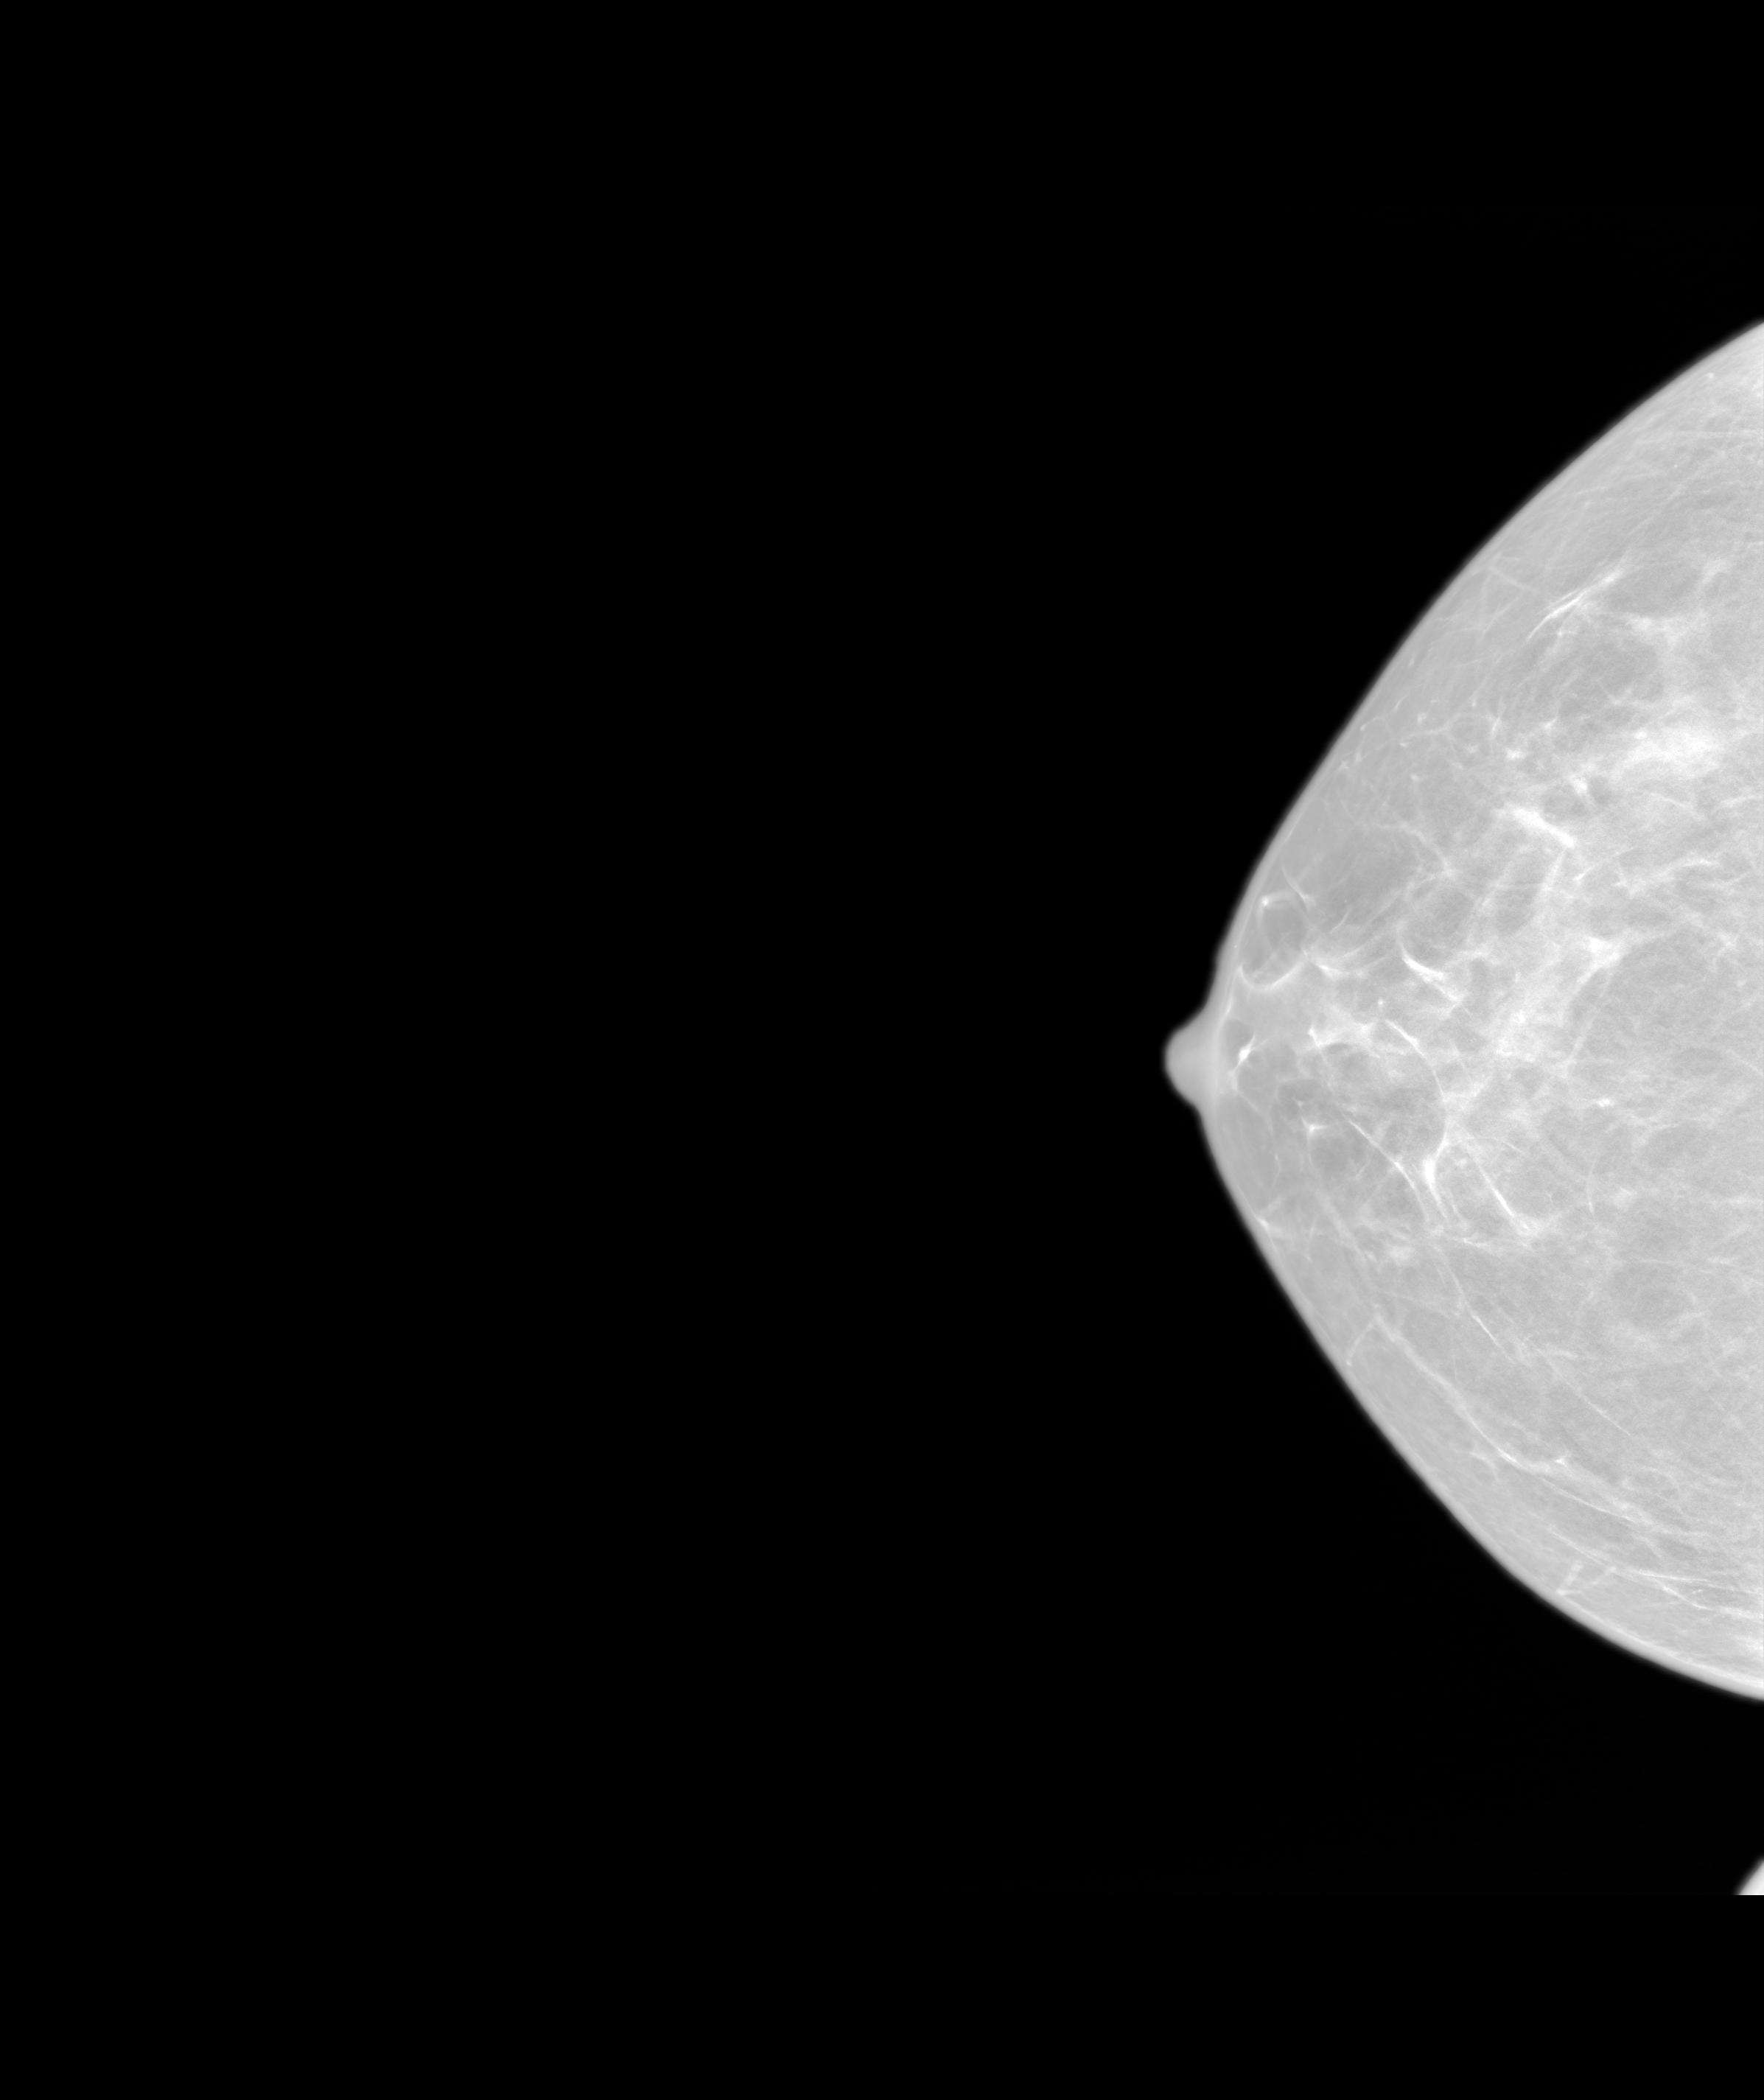
Synthetic 2-D view generated from a tomosynthesis acquisition (not an FFDM exposure); right breast; CC view; annual screening mammography examination; system: SenoIris_1SP1.1(421). Female patient, age 43 years.
Breast density at the screening exam (both breasts): scattered fibroglandular densities (BI-RADS density category b). Final BI-RADS category for the screening round (tomosynthesis exam, both breasts): category 1. Recall: no recall after this screen.